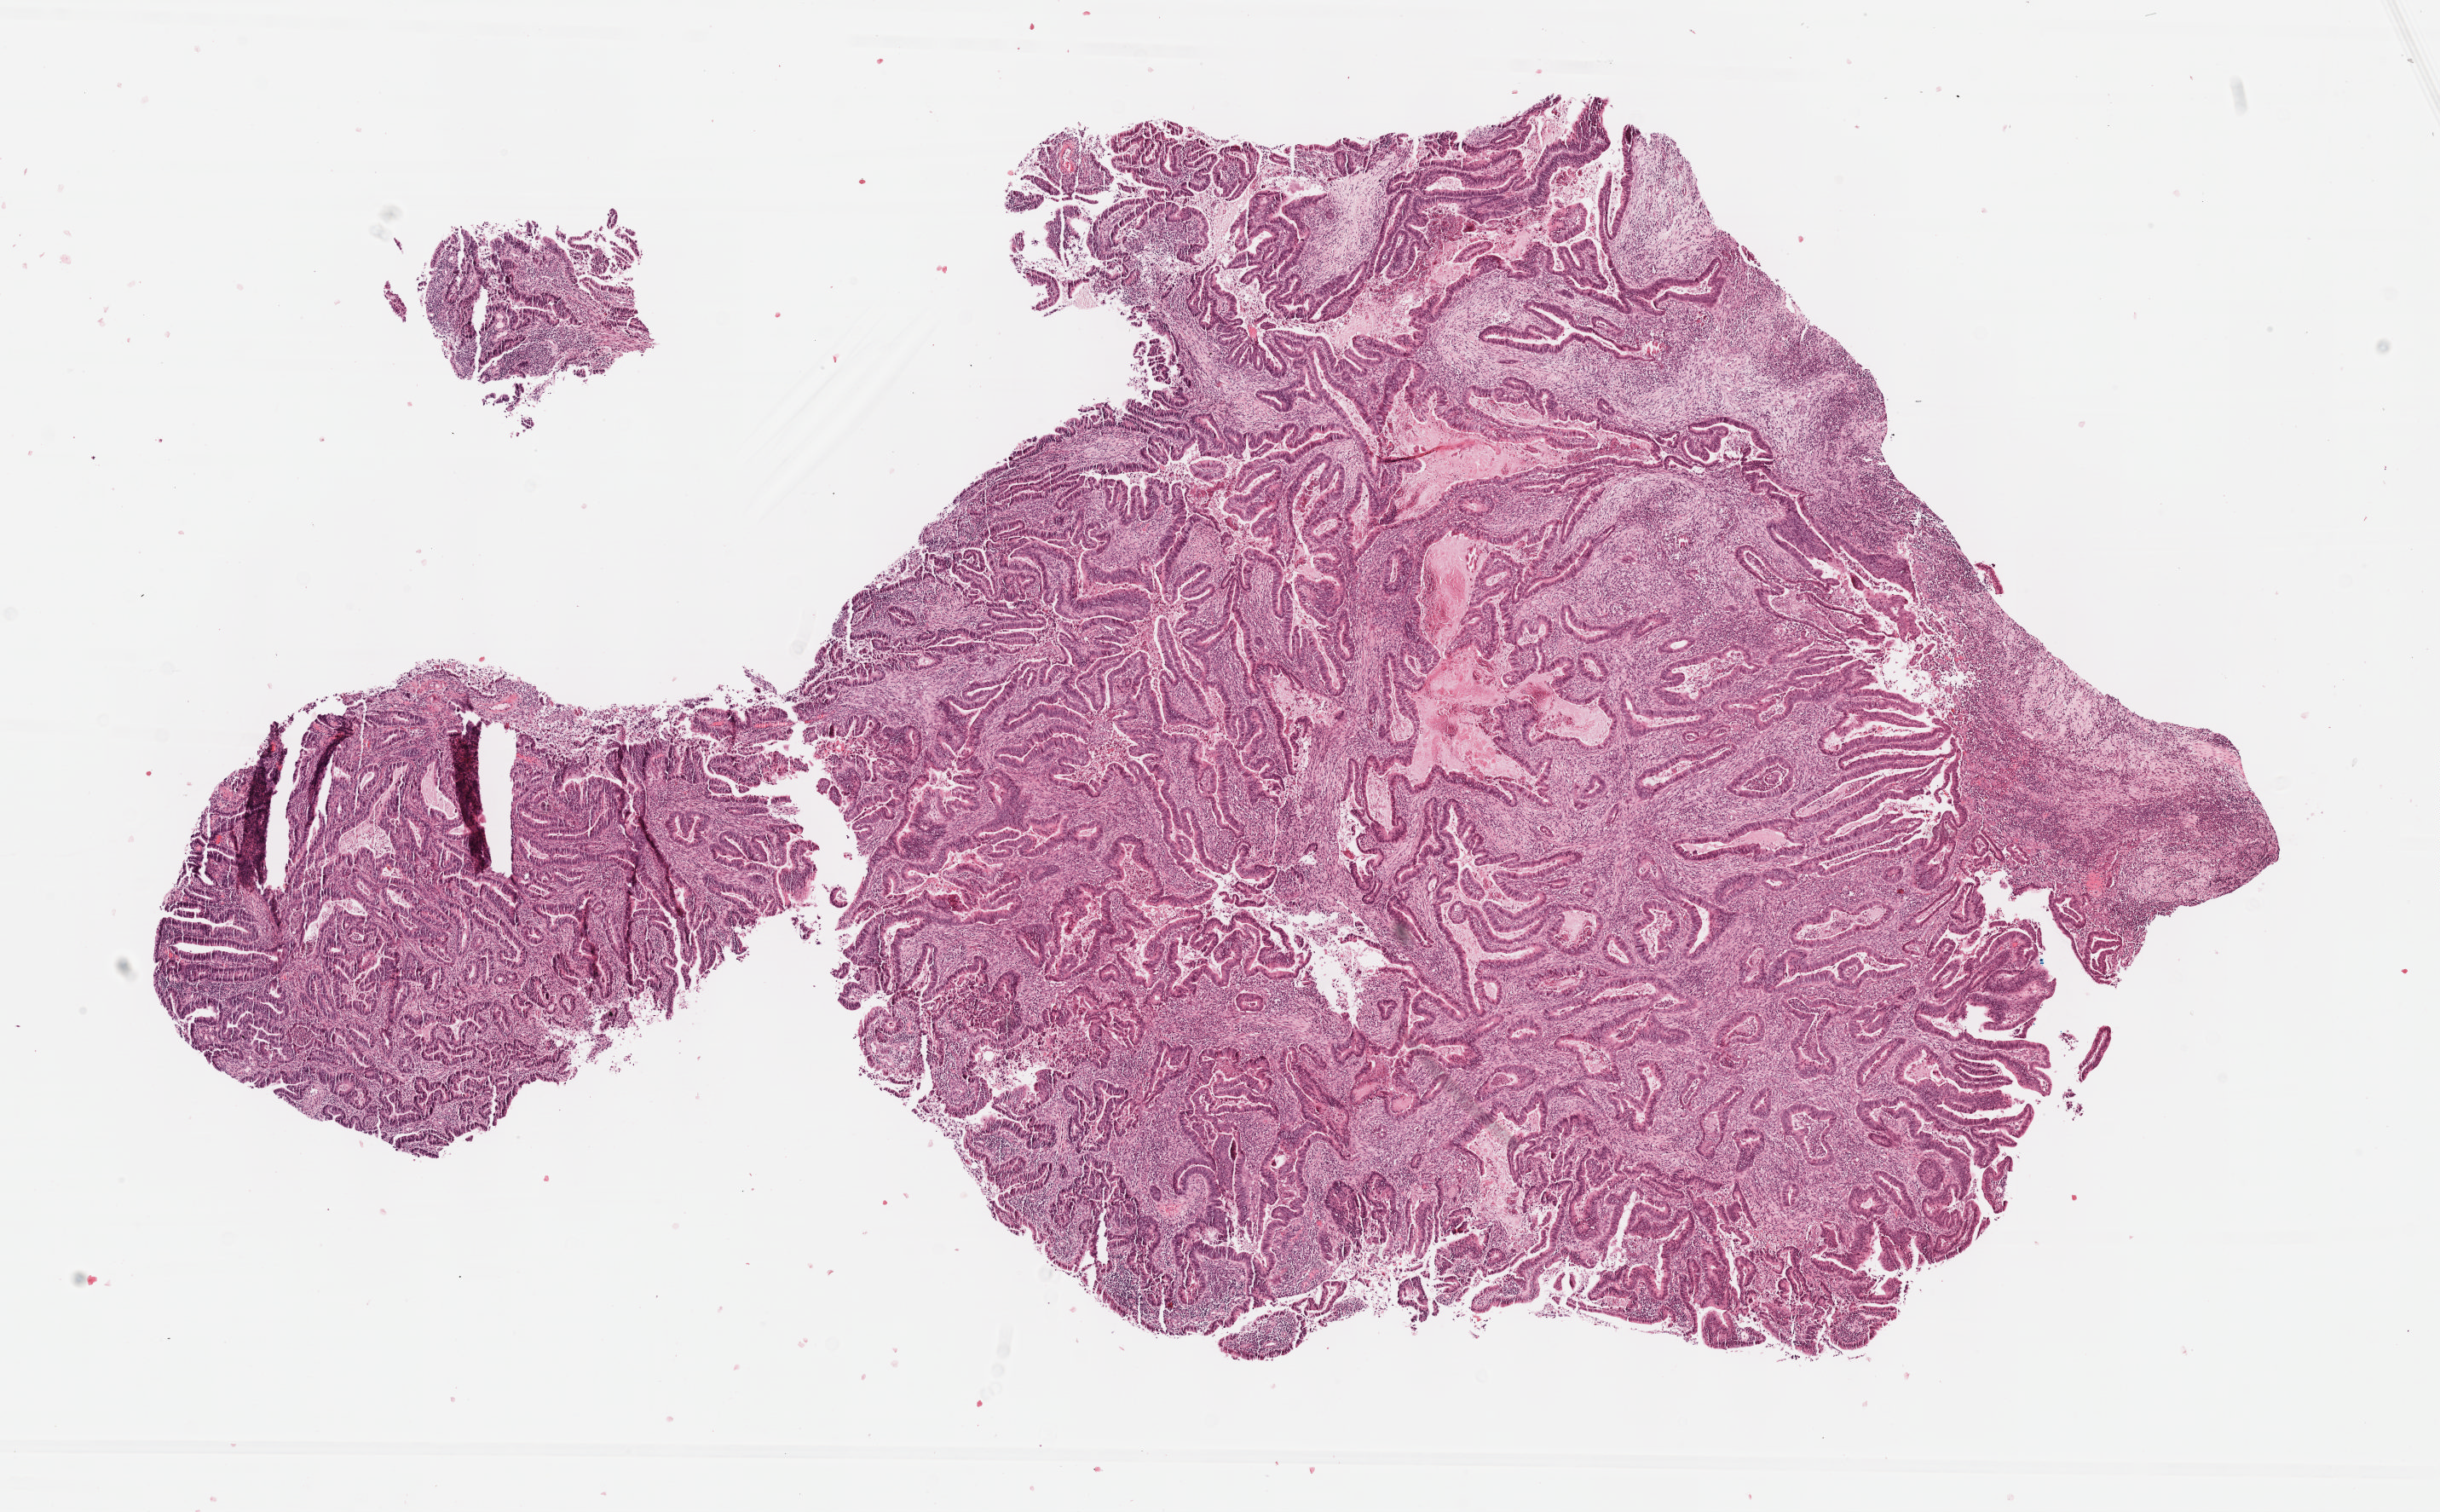
Whole-slide histology image, H&E-stained, a low-resolution overview of the entire scanned area, about 11.6 x 7.2 mm, formalin-fixed paraffin-embedded (FFPE) diagnostic section, primary tumour sample from the colon. Female patient; age at initial diagnosis 80 years.
Pathologic diagnosis: Adenocarcinoma, NOS. AJCC pathologic stage: IIA.